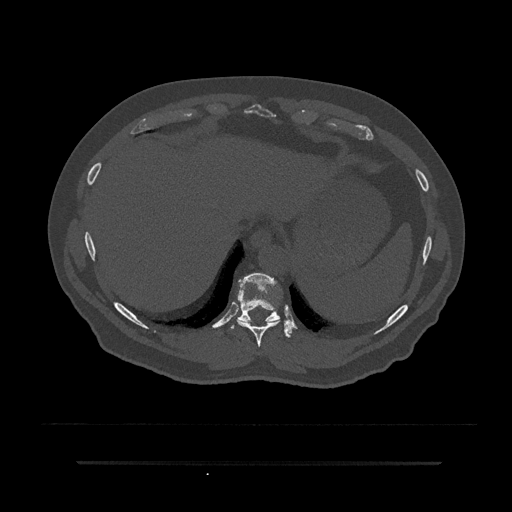
CT including the spine, one axial slice; position 354 of 797 along the scan axis; reconstruction kernel Br40s/3; bone window (W 1800 / L 400 HU); 0.5 mm slice thickness; 512 × 512 image matrix. Patient: male, 59 years. From the clinical record (not read from this slice): primary cancer: bile ducts; vertebrae with lytic lesions (as recorded): T10.
Outlined on this slice (semi-automatic segmentation, software-assisted and operator-edited):
- T10 vertebra: box from (x=231, y=273) to (x=293, y=337) px
- T9 vertebra: (x=240, y=282)–(x=280, y=347)